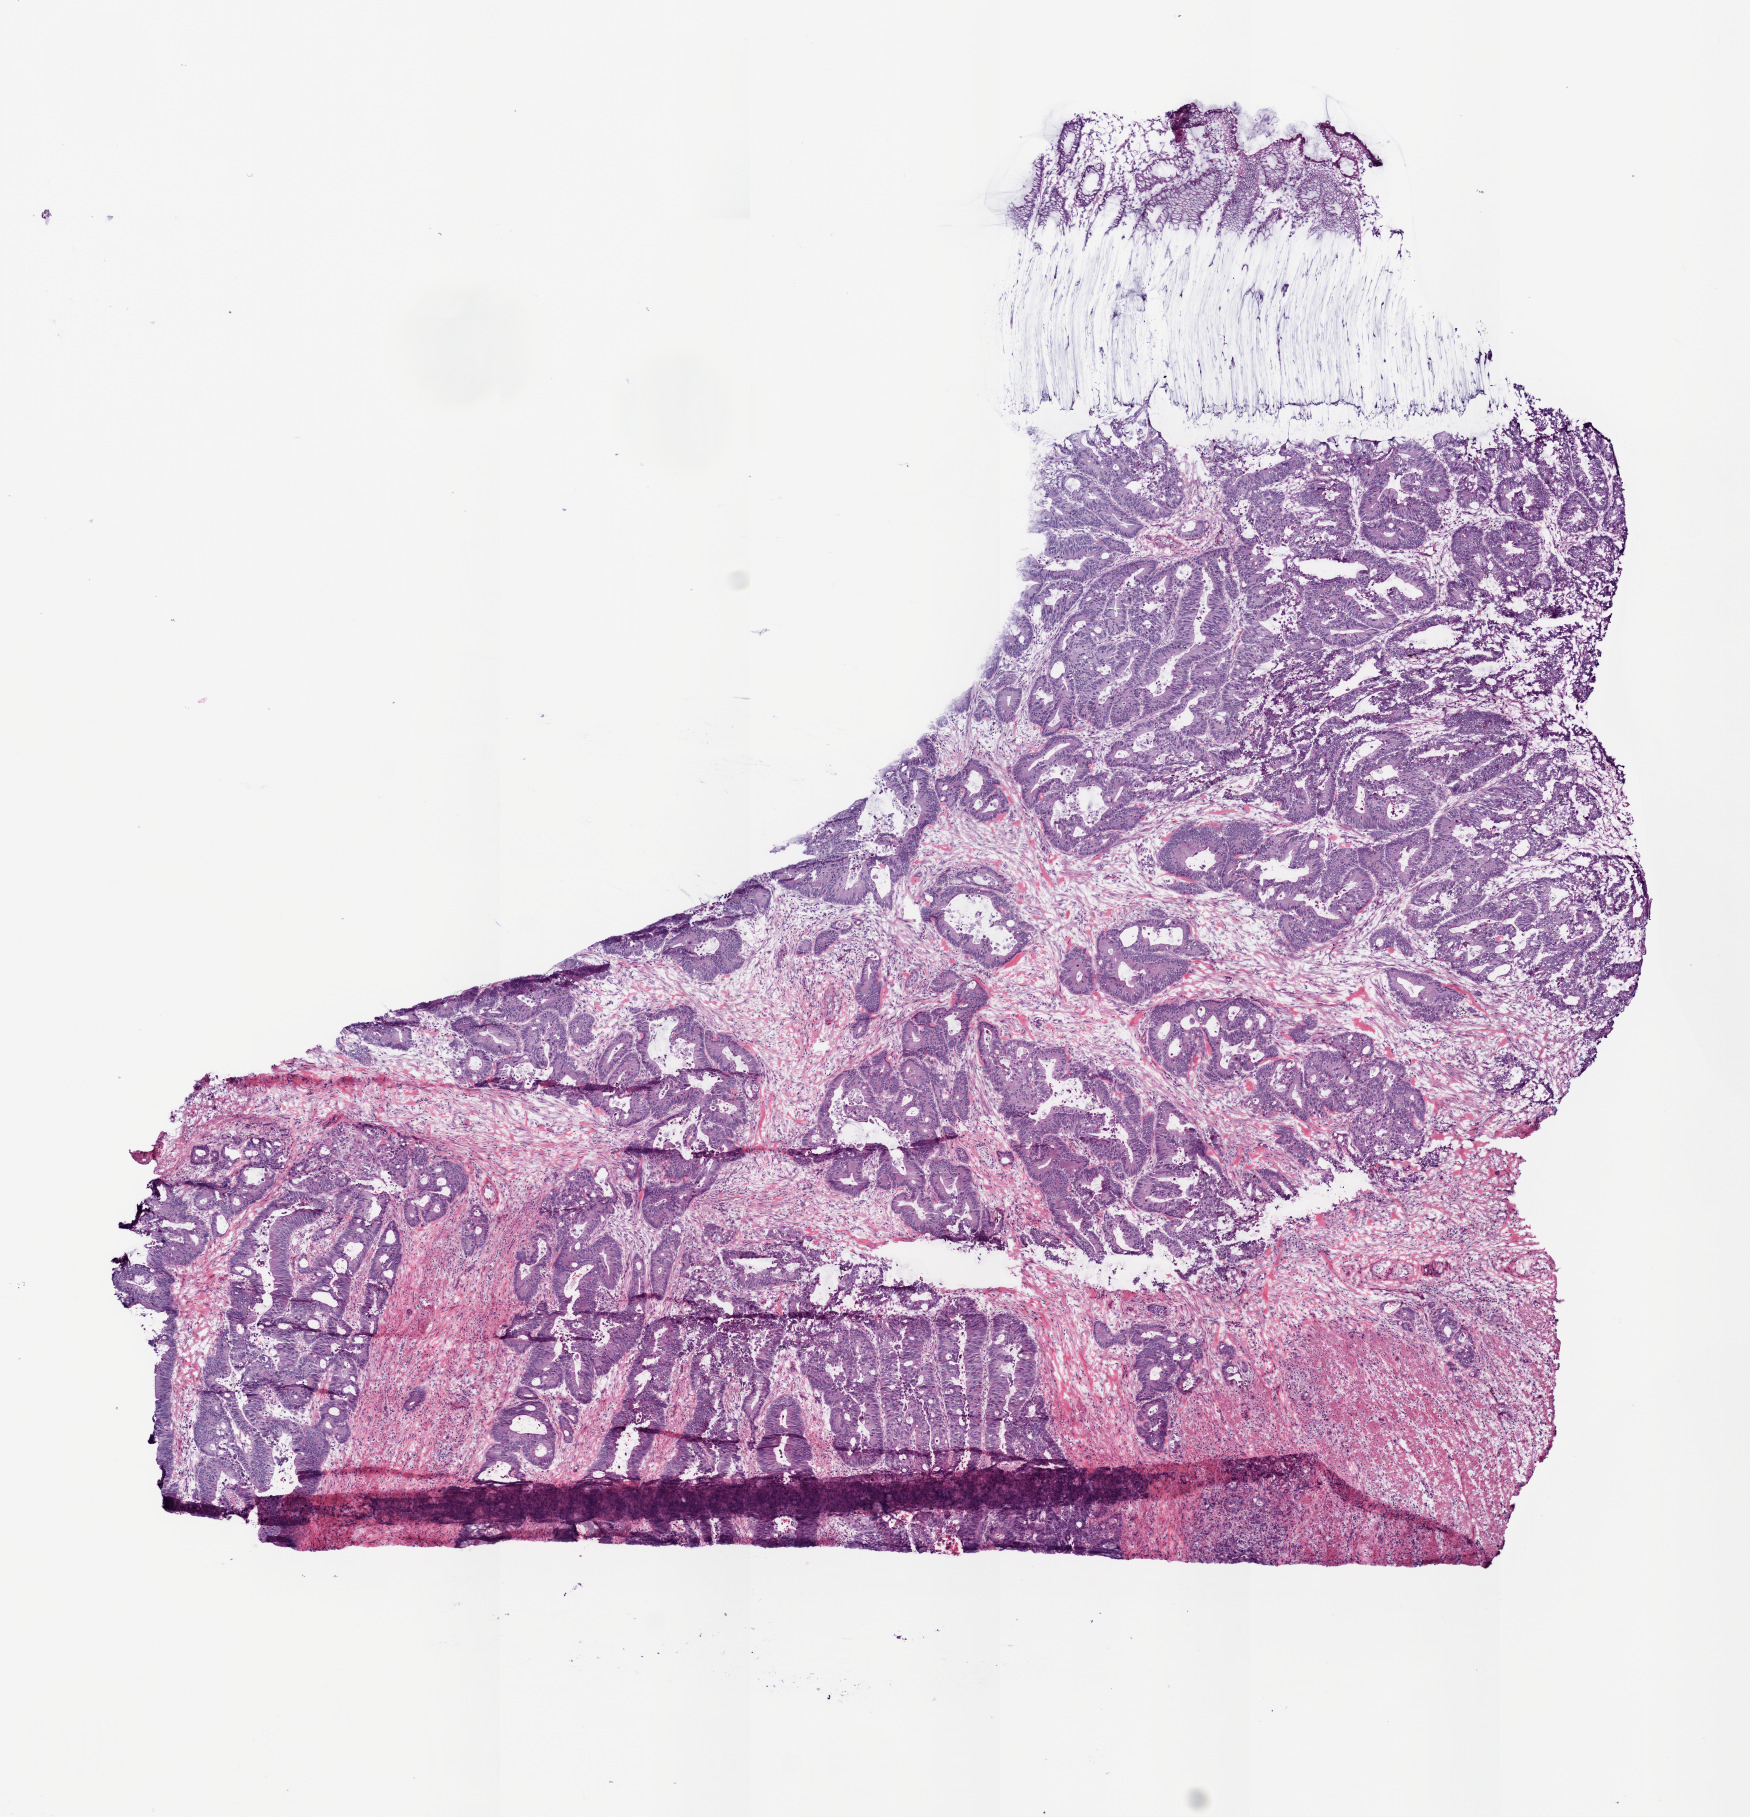
Whole-slide histology image, H&E, low-resolution overview of the scanned area, about 7.0 x 7.3 mm (from a 20x scan), frozen section from the top of the tissue portion, rectum, primary tumour sample. Female, age 69 years at initial diagnosis. Pathologist review of this section (percent, as recorded): tumour cells 72%, tumour nuclei 75%, normal cells 5%, stromal cells 20%, necrosis 3%.
Lymph nodes positive (case pathology): 3 of 35 examined. AJCC pathologic stage: IIIB. Diagnosis: Adenocarcinoma, NOS.